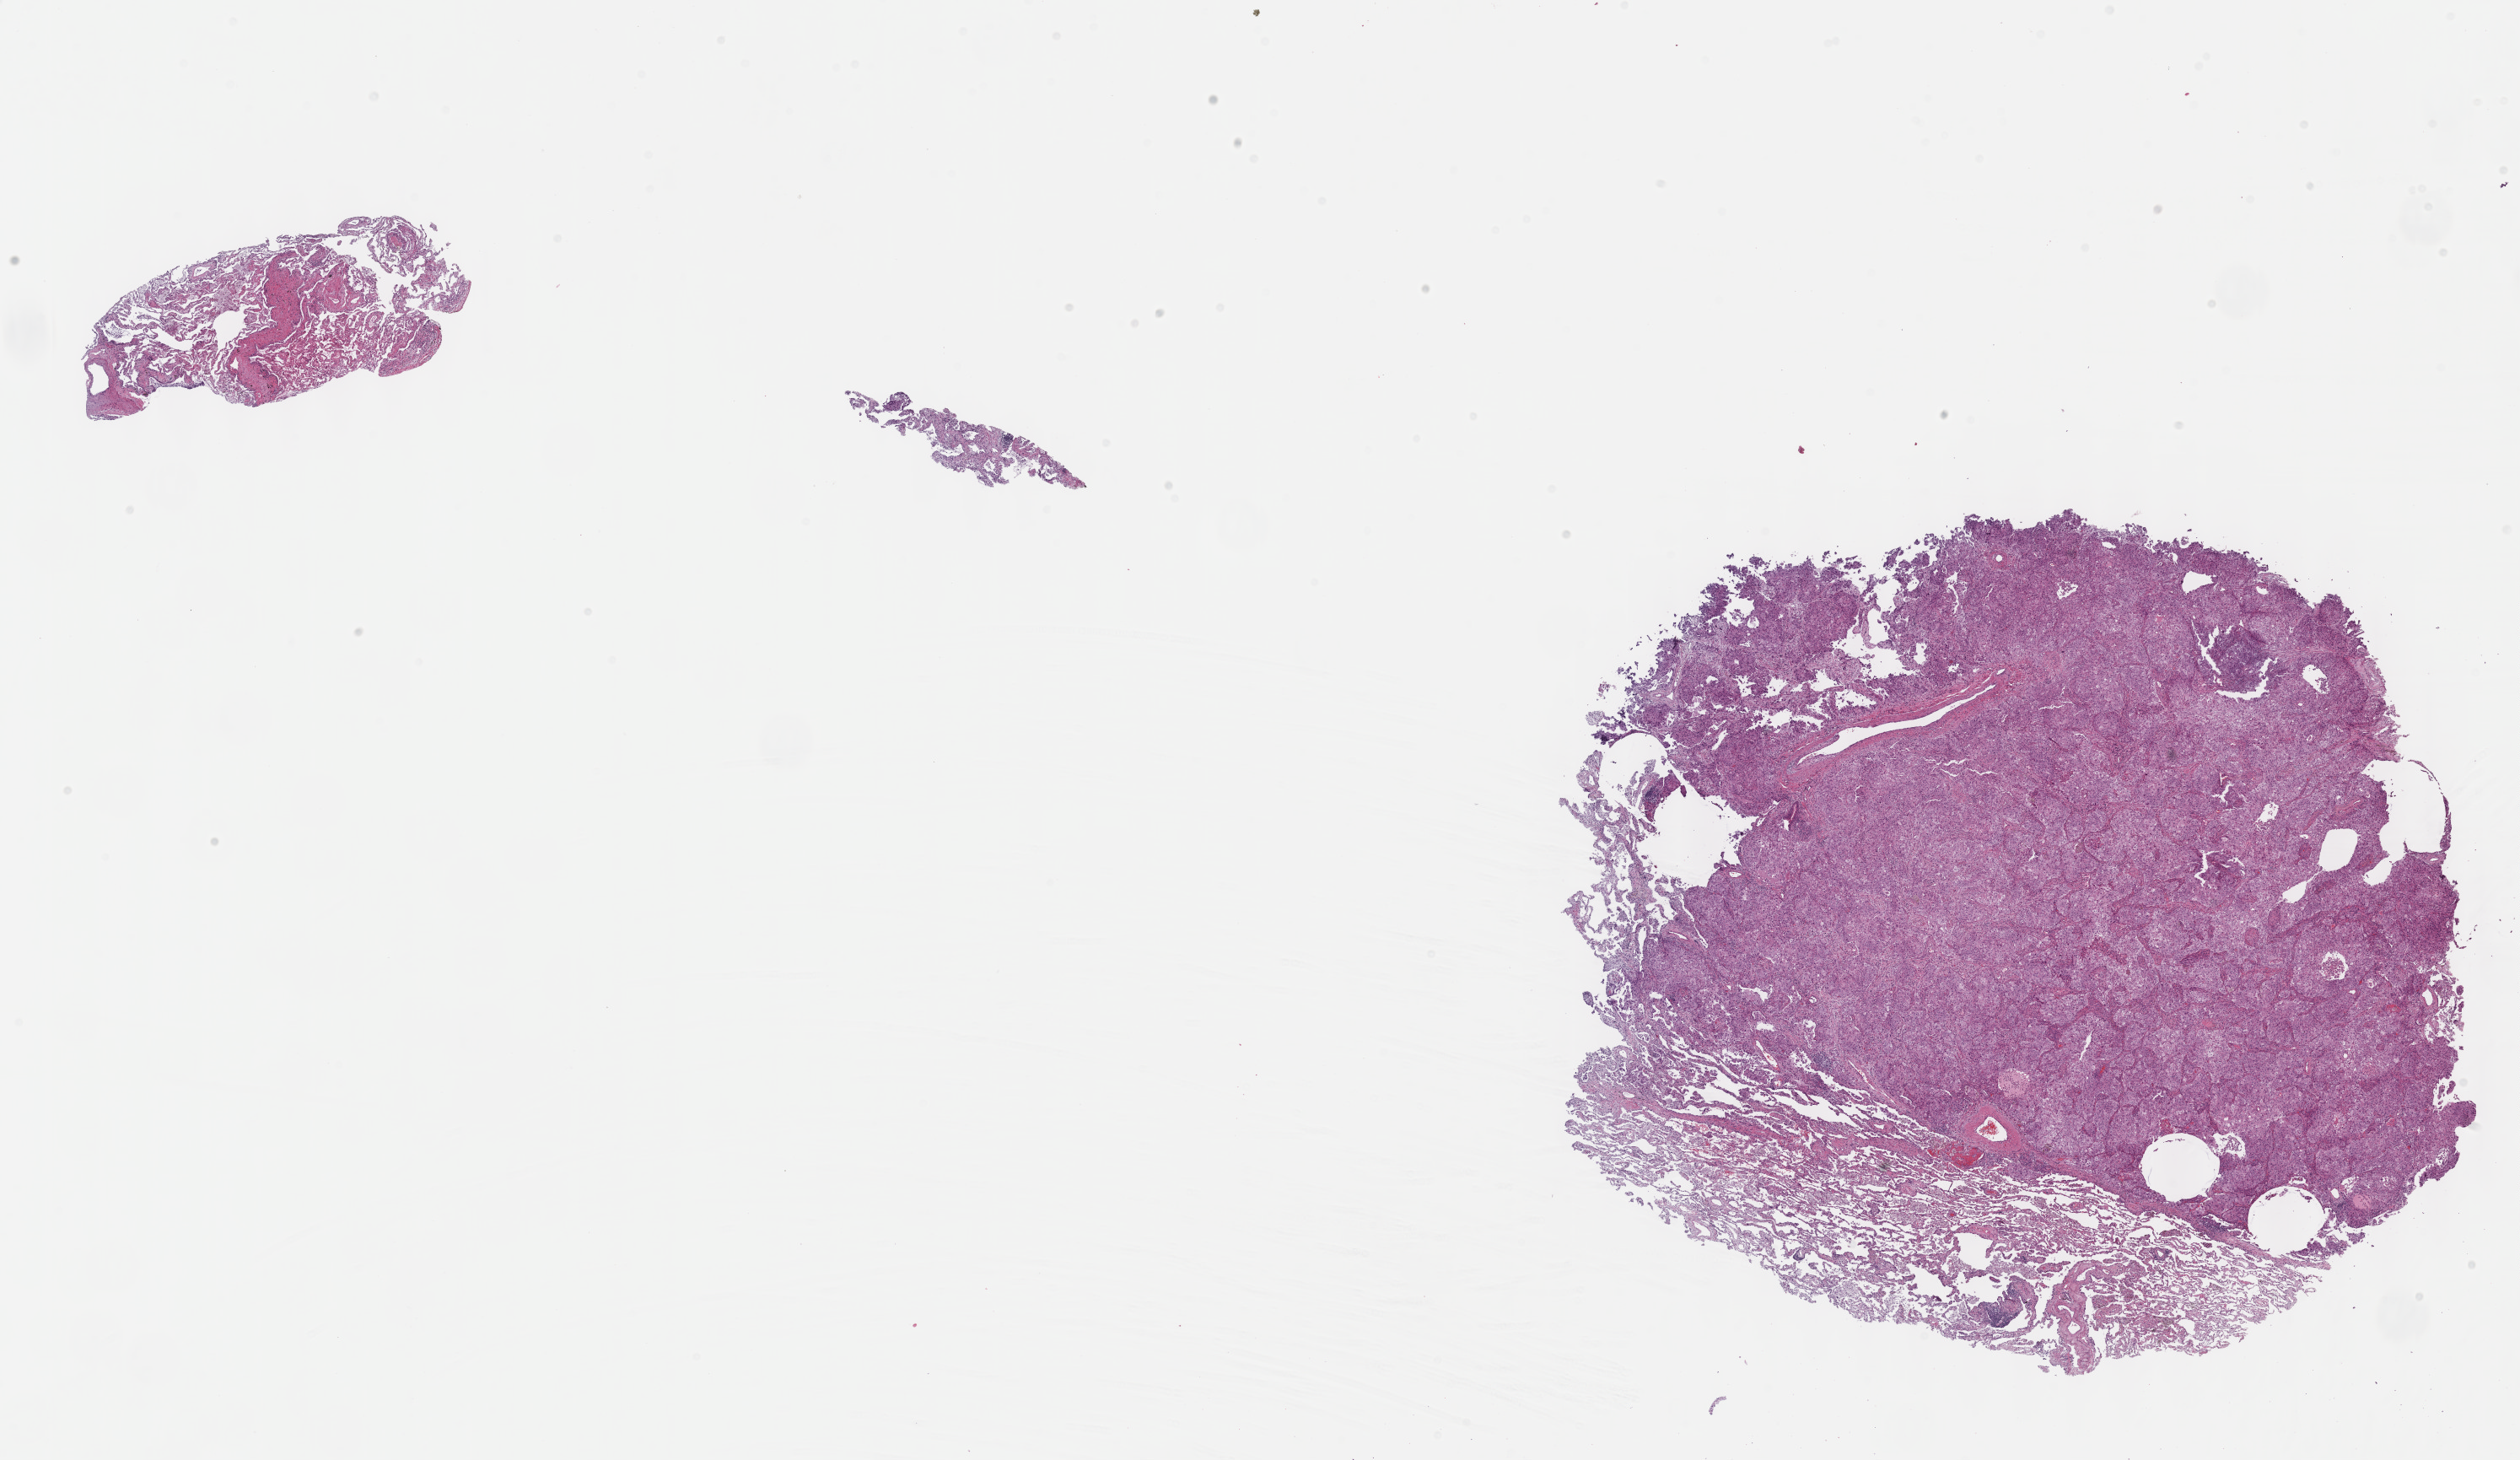
Hematoxylin and eosin (H&E) stained whole-slide image, shown as a low-resolution overview of the whole scanned area (about 24.1 x 14.0 mm, acquisition: 40x scan), formalin-fixed paraffin-embedded (FFPE) diagnostic section, primary tumour sample from the lung. Female, age 69 years at initial diagnosis.
AJCC pathologic stage: IB. TNM: T1b N0 M0. Histologic diagnosis: Squamous cell carcinoma, NOS (upper lobe, lung).